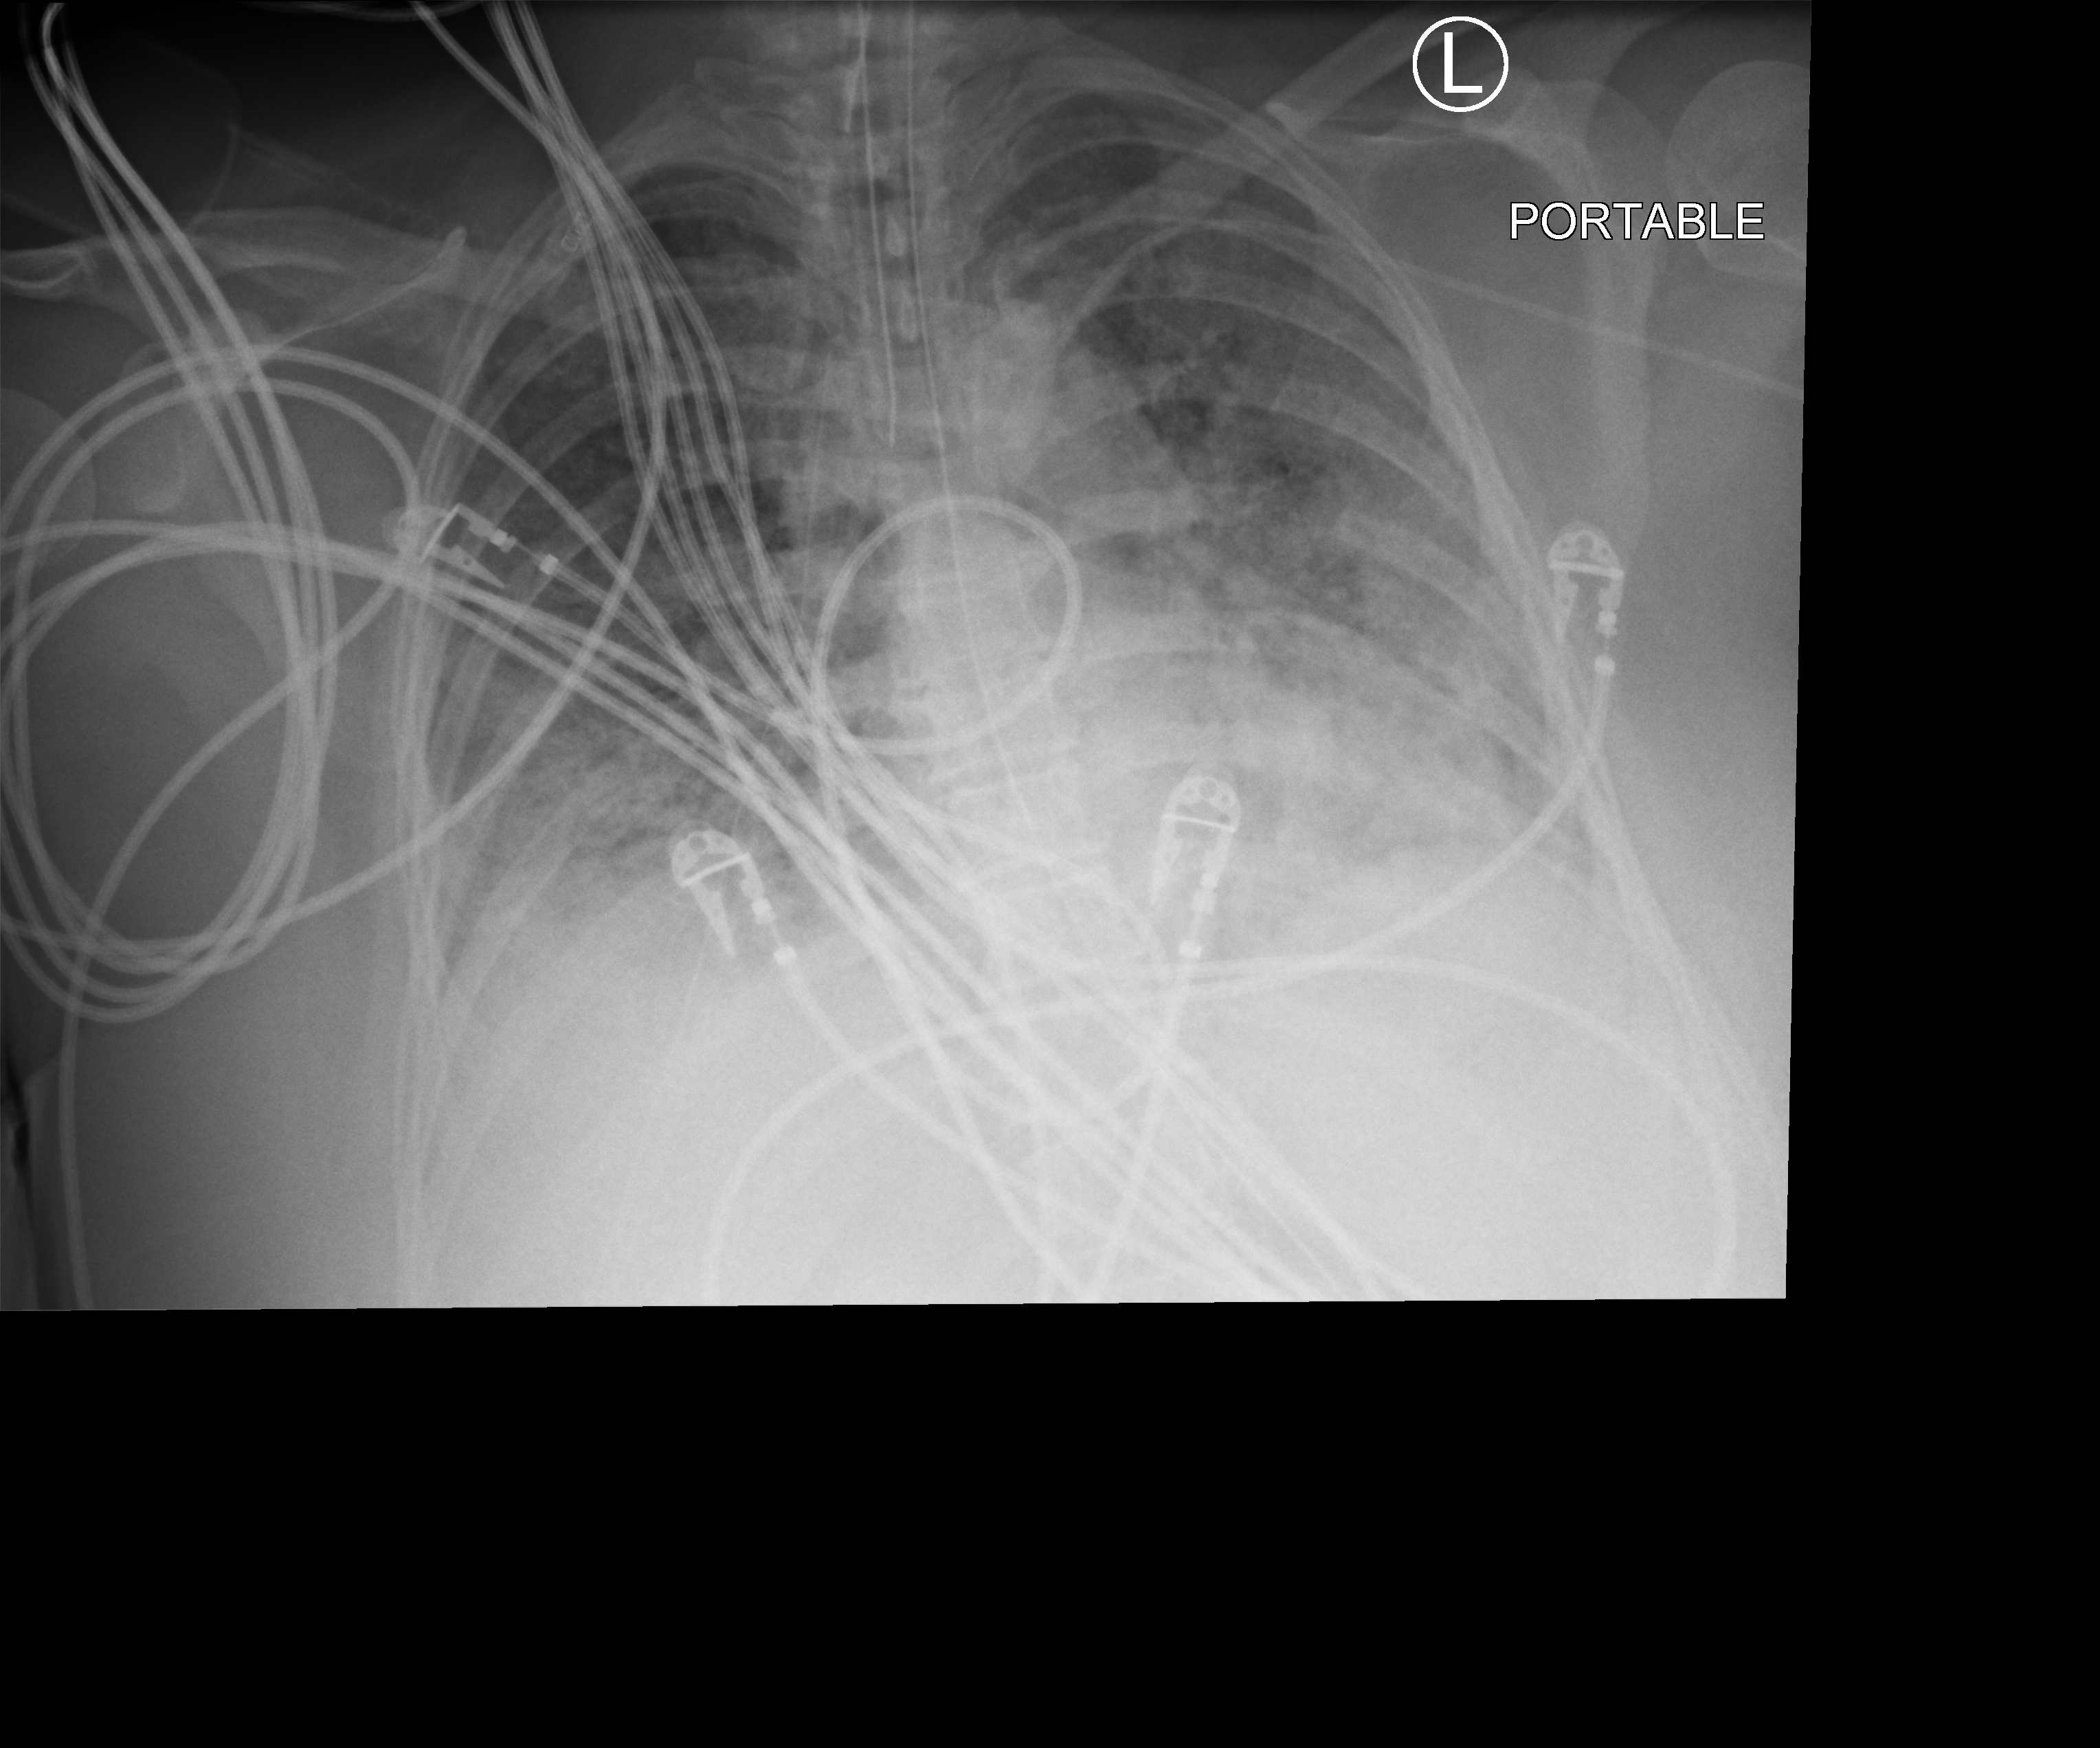
Chest X-ray (portable); anteroposterior (AP) projection. Patient hospitalised with COVID-19; female, aged 18–59 years.
Hospital-stay facts (about this admission, not read from this image; timing relative to this image not recorded): admitted to intensive care during this hospital stay: yes; mechanically ventilated during this hospital stay: yes.